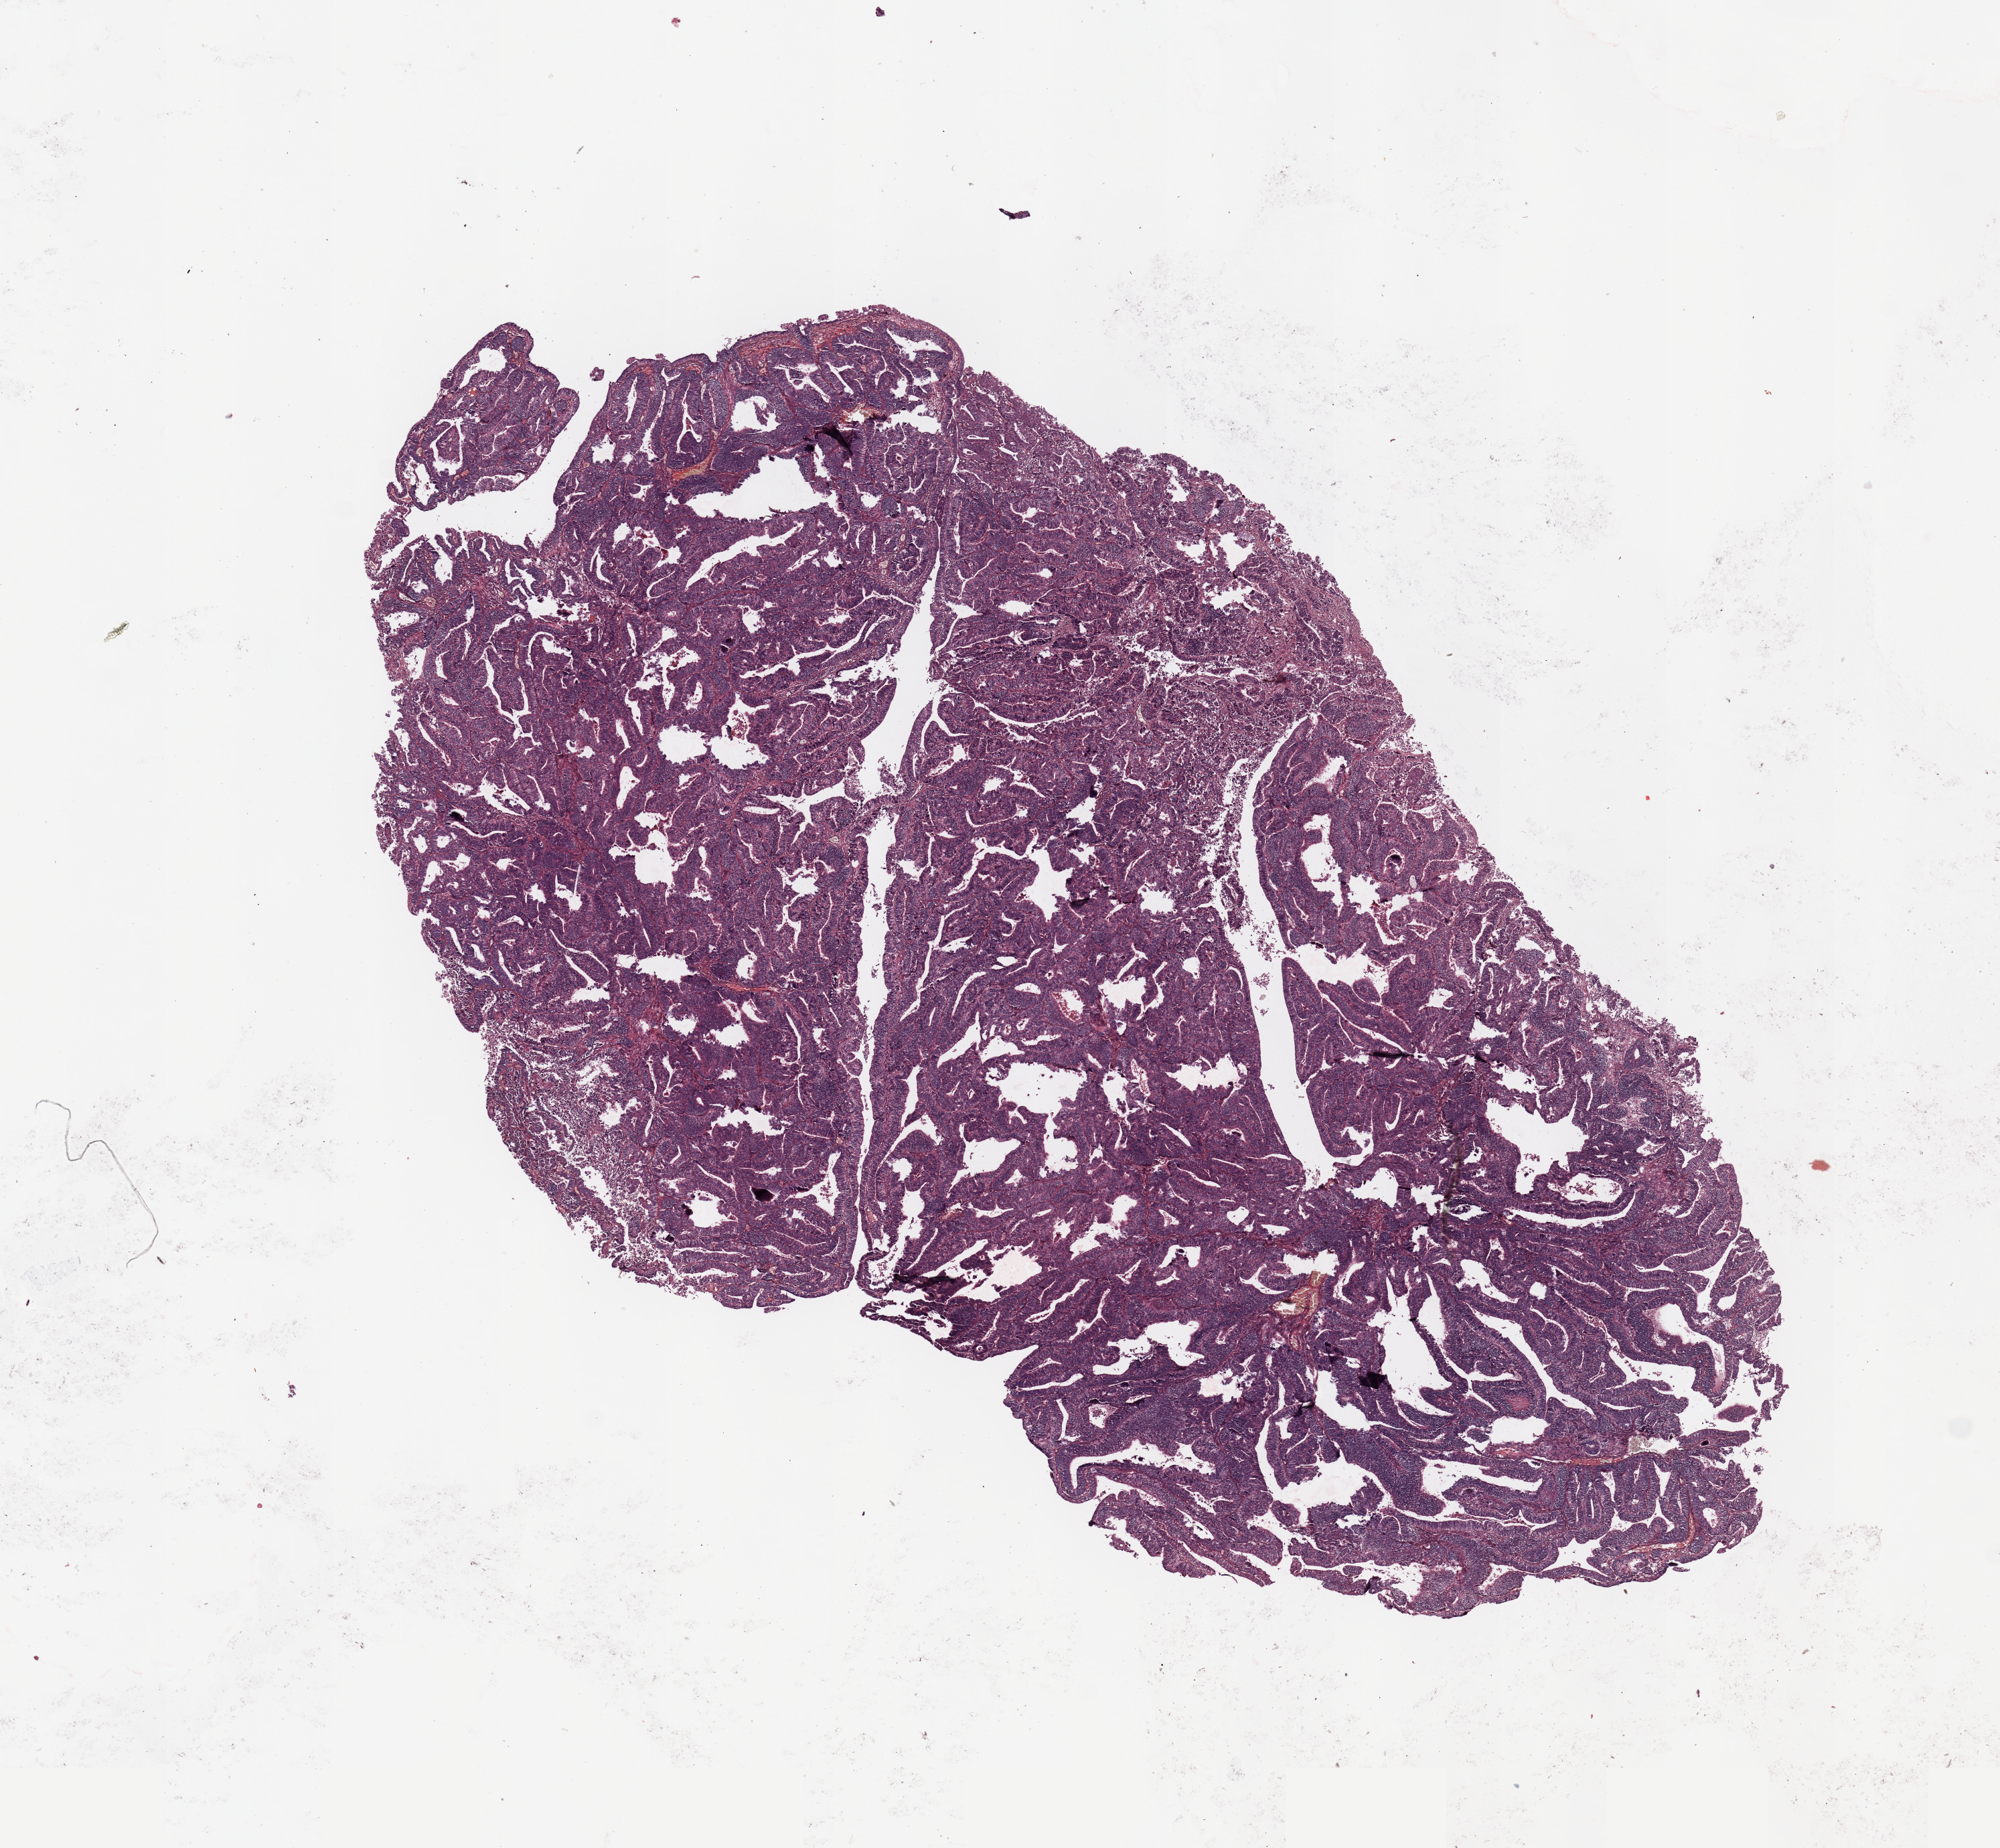
Hematoxylin and eosin (H&E) stained whole-slide image — low-resolution overview of the scanned area, about 11.8 x 10.9 mm. Tumour tissue sample, uterus. Patient: female, age 66 years. Histologic grade: G1 (well differentiated).
AJCC pathologic stage: I. Diagnosis: Endometrioid adenocarcinoma, NOS.